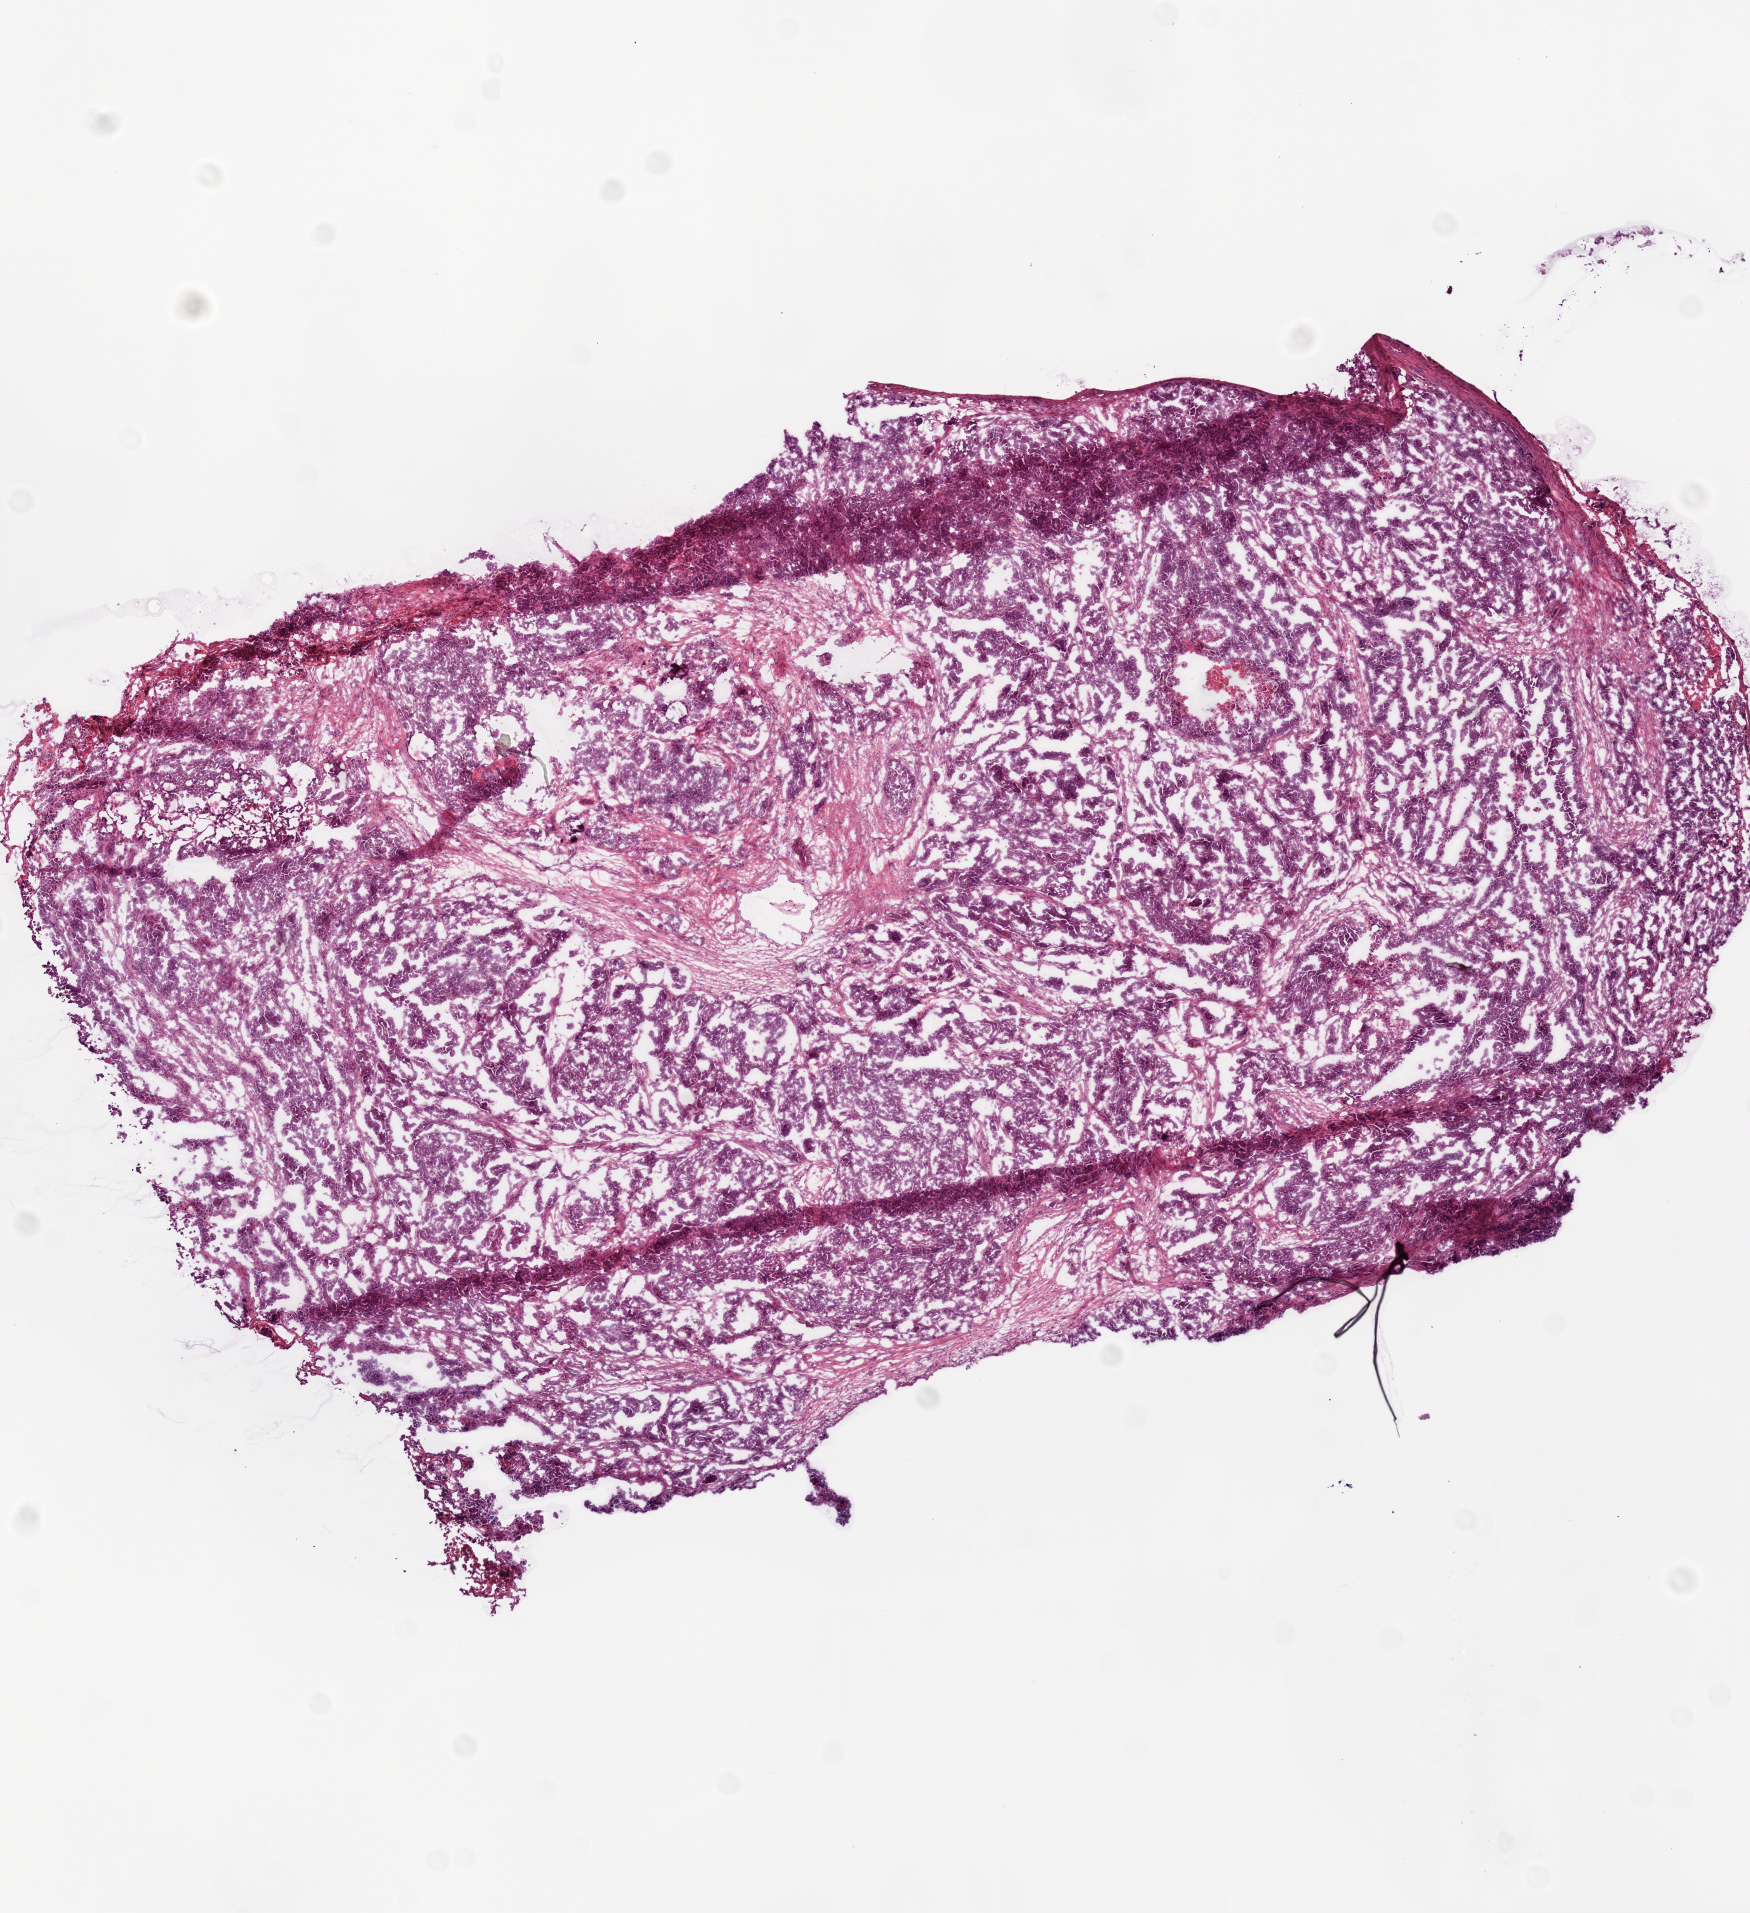
Whole-slide histology image, Hematoxylin and eosin (H&E) stained, whole scanned area (about 7.0 x 7.7 mm) shown as a low-resolution overview, frozen section, primary tumour sample from the ovary. Patient: female, age at initial diagnosis 77 years. Histologic grade: G3 (poorly differentiated). Slide review estimates, as recorded: tumour cells 80%, tumour nuclei 80%, normal cells 0%, stromal cells 10%, necrosis 10%. Inflammatory infiltration, as recorded: lymphocyte infiltration 0%, monocyte infiltration 0%, neutrophil infiltration 10%.
FIGO stage: IIIC. Diagnosis: Serous cystadenocarcinoma, NOS.